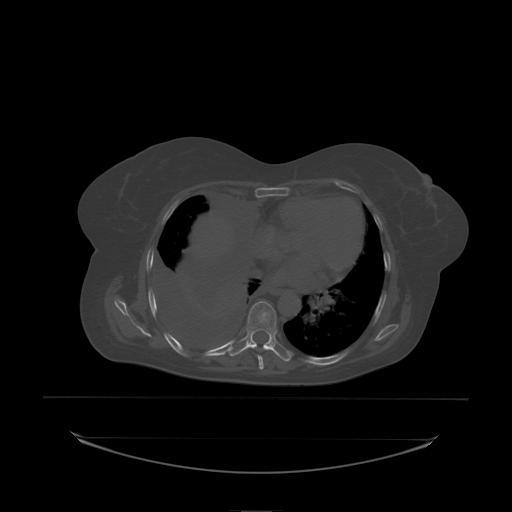
CT including the spine, one axial slice; slice 135 of 242 in the series (ordered by position); bone window (W 1800 / L 400 HU); 512 × 512 image matrix, field of view 500 × 500 mm. Patient: female, 53 years. From the clinical record (not read from this slice): primary cancer: lung; vertebrae with lytic lesions (as recorded): T7, L1.
Outlined on this slice (semi-automatic segmentation, software-assisted and operator-edited):
- T8 vertebra: bounding box <246,301,278,338> (left, top, right, bottom; pixels)